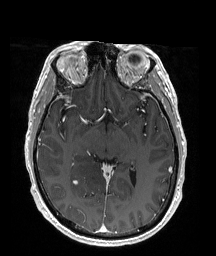
Brain MRI from a brain-tumour surgery series, one axial slice; position 104 of 176 along the scan axis; T1-weighted post-contrast; 1 mm slice thickness; 216 × 256 image matrix, field of view 211 × 250 mm. Case-level facts recorded for this patient, not image findings: histopathology: Oligodendroglioma; WHO grade: 2; IDH mutation: yes.
Structures marked on this image (outlined manually by an expert reader):
- tumour: bounding box [x1, y1, x2, y2] px = [70, 150, 111, 205]